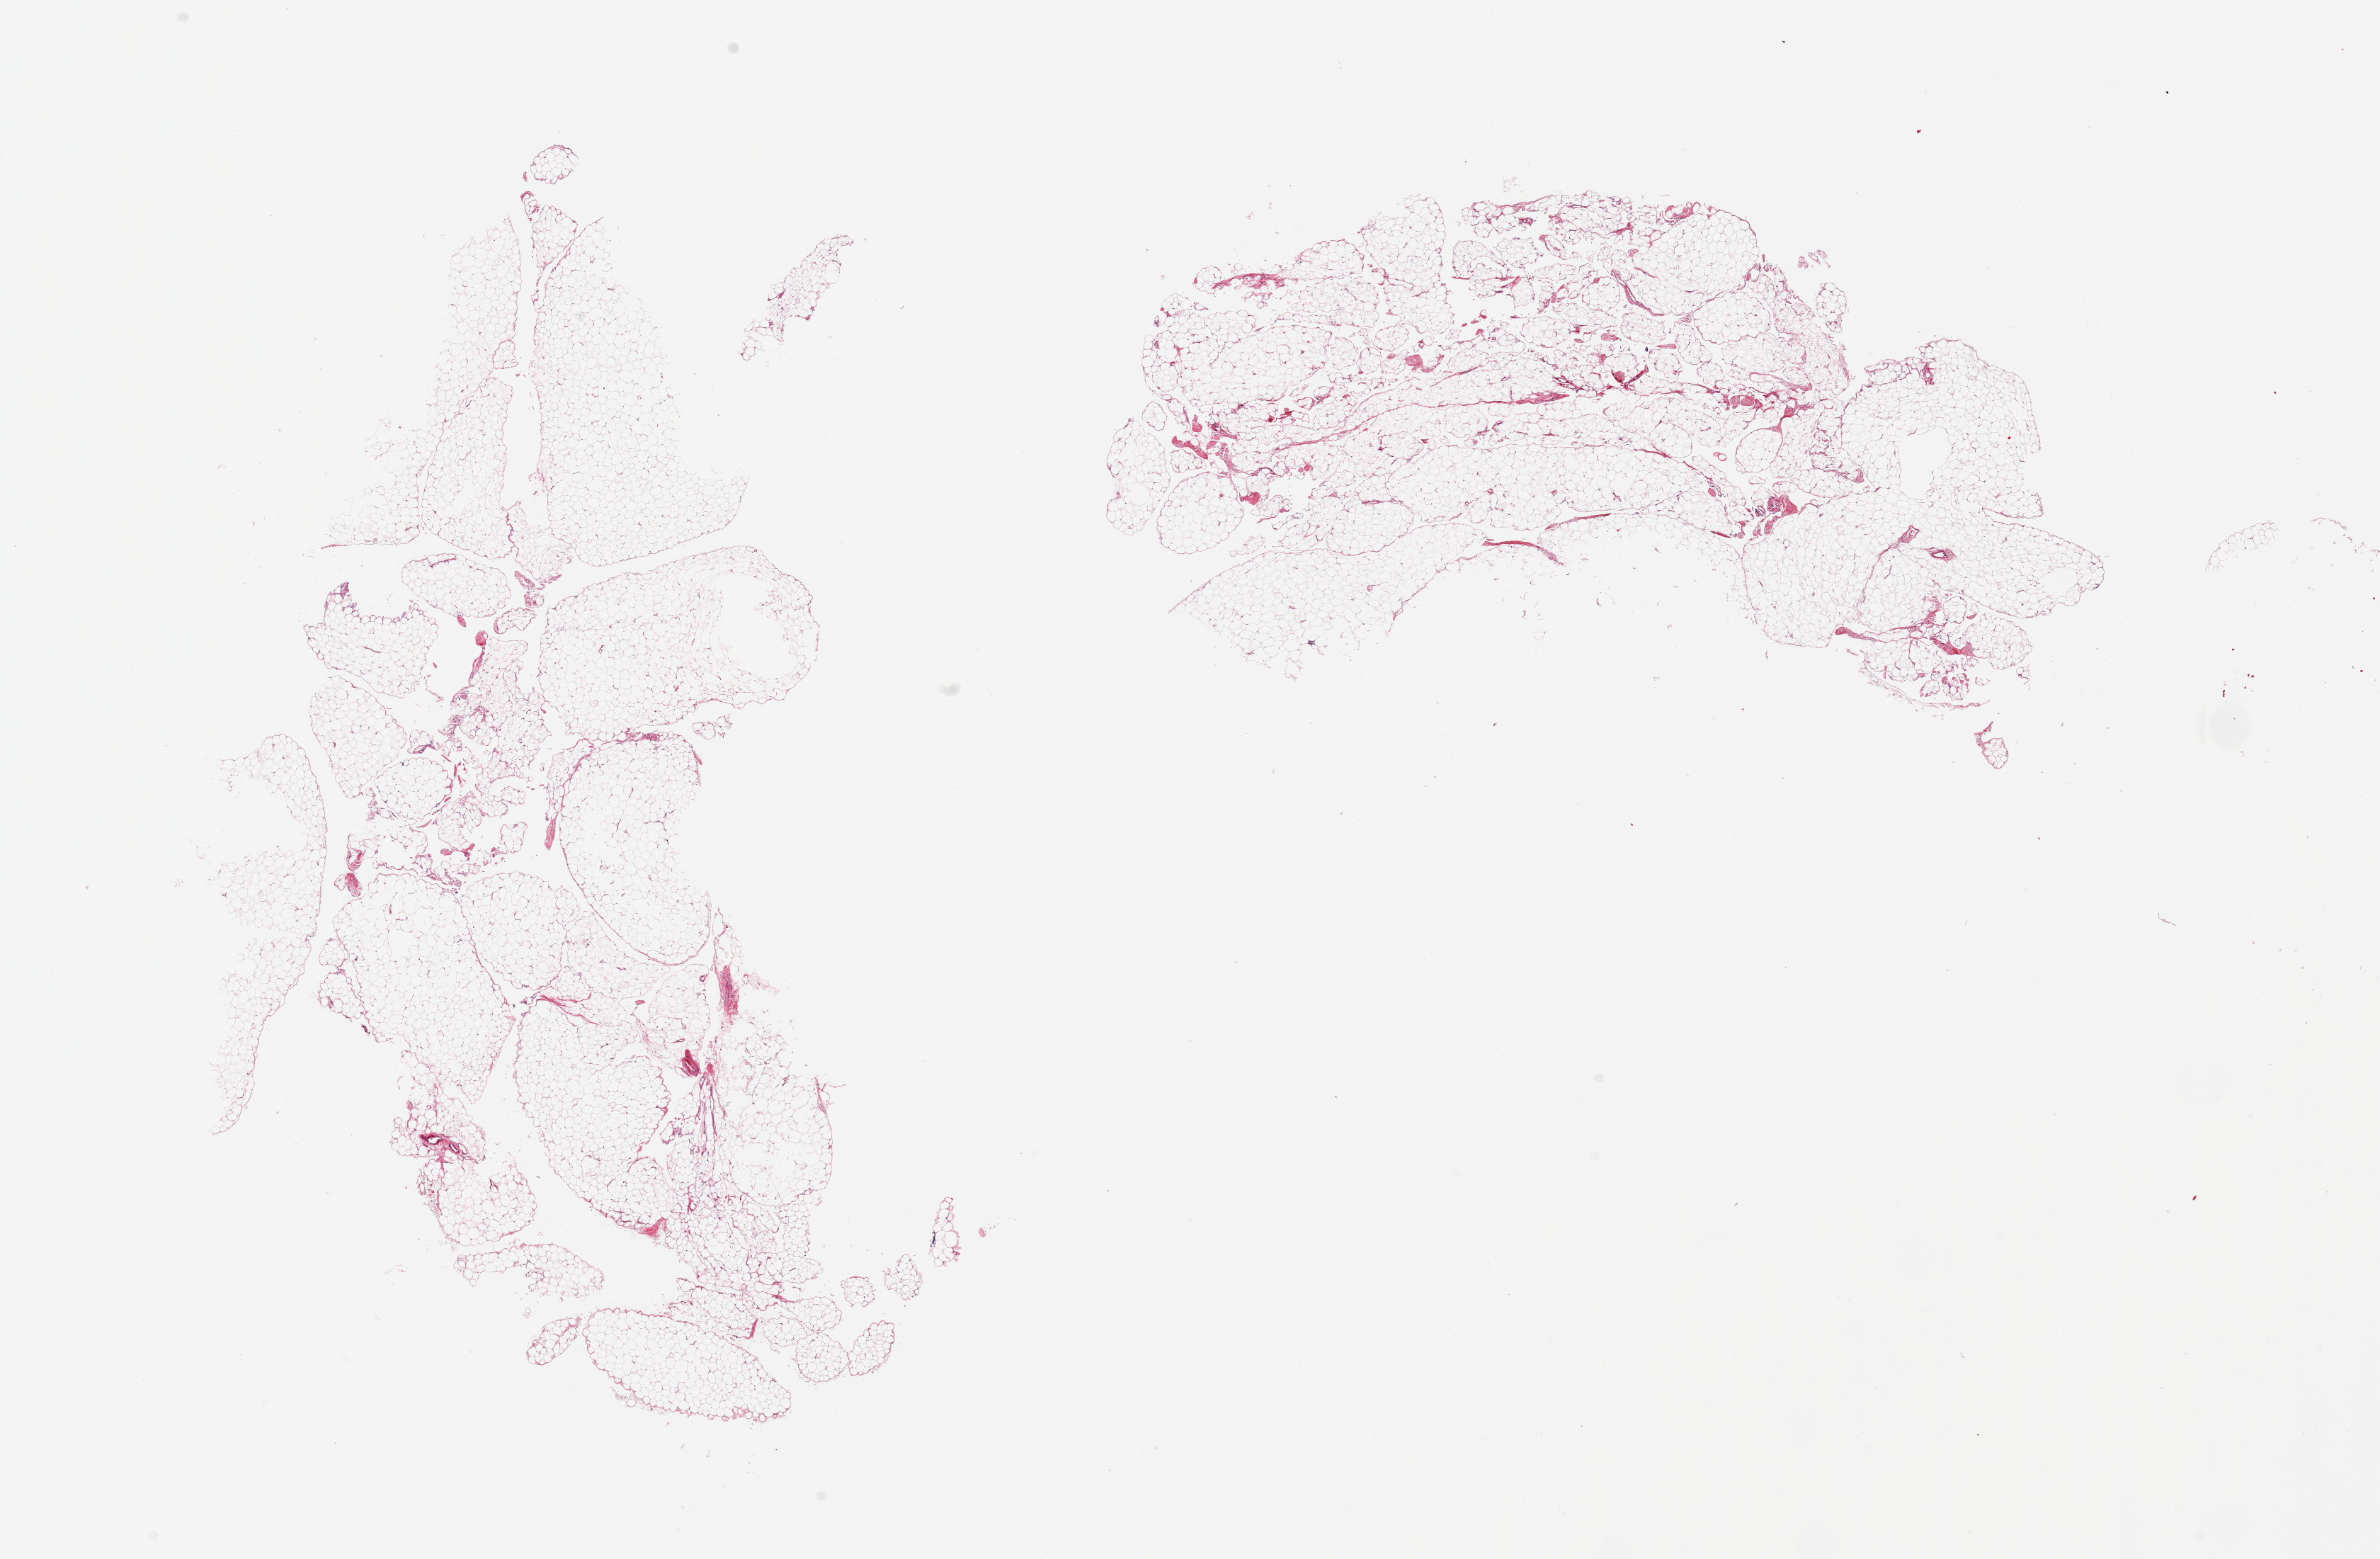
Whole-slide image, haematoxylin and eosin stain, brightfield, low-resolution overview of the scanned area, about 26.6 x 17.4 mm (acquisition: 20x scan); PAXgene-fixed paraffin-embedded (PFPE) section; section of omentum (target tissue); tissue donor sample. Donor: male.
Reviewer comment on this tissue sample: 2 pieces.